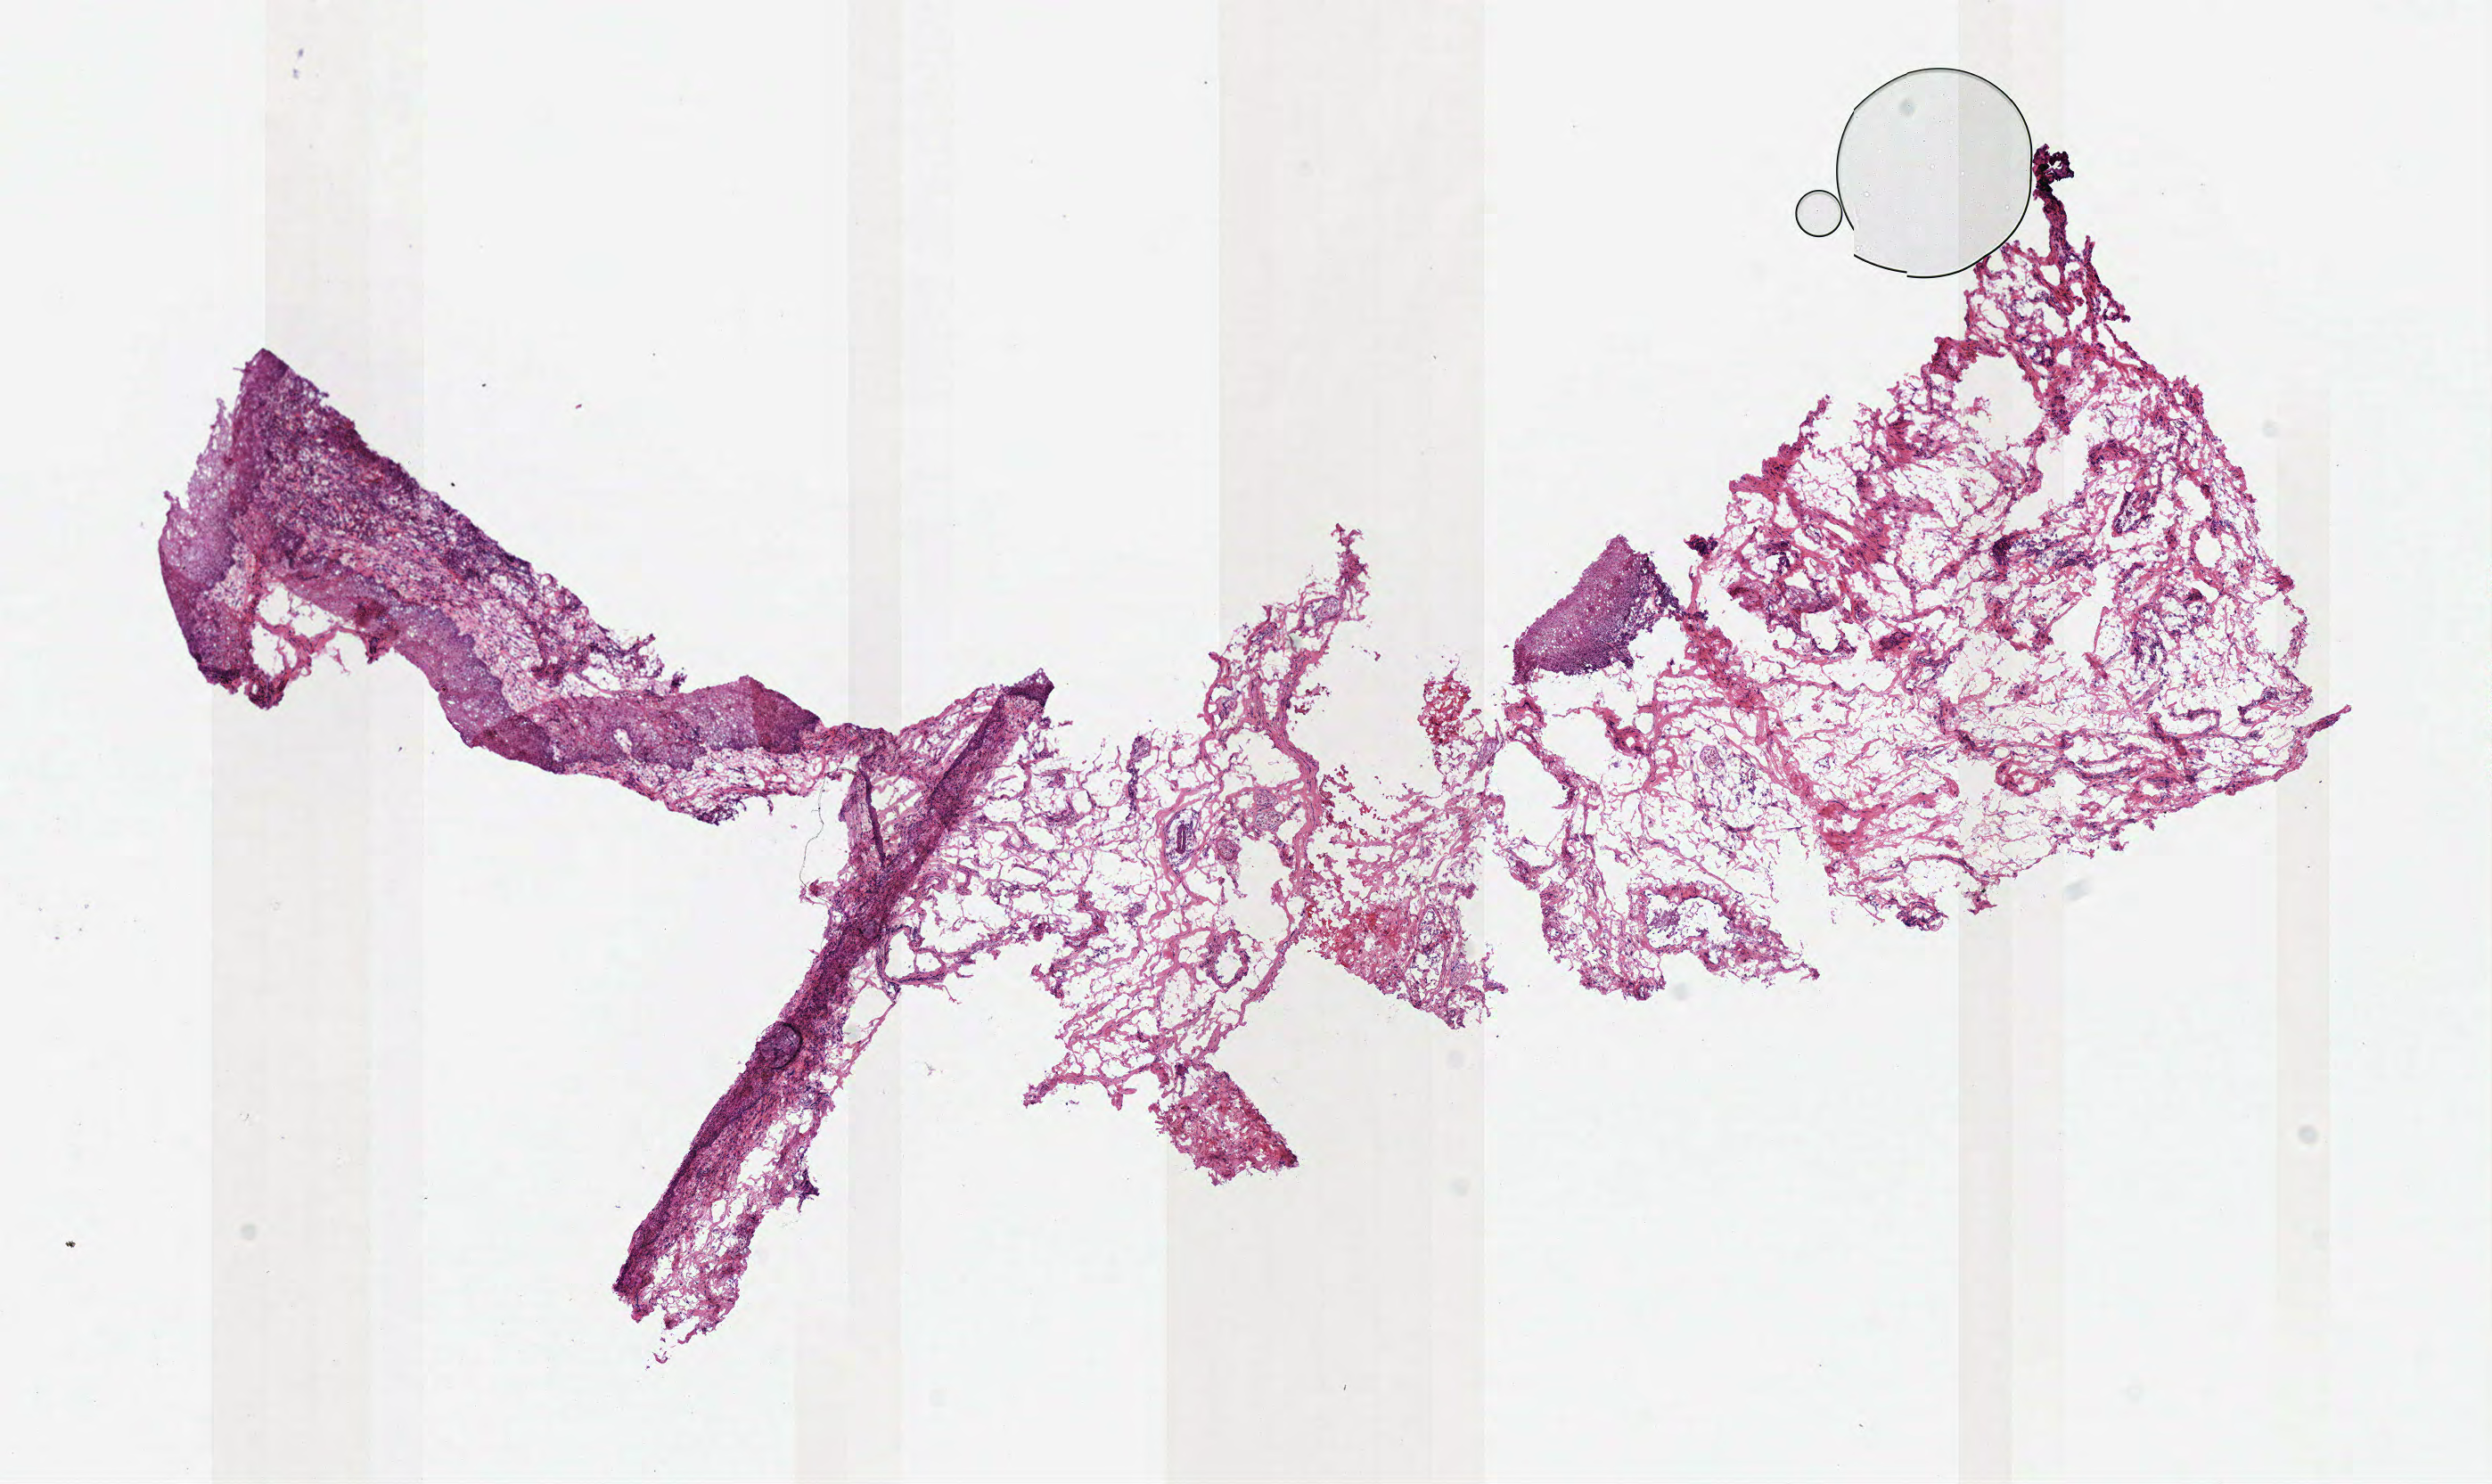
Digitized Hematoxylin and eosin (H&E) stained tissue section (whole slide), whole scanned area (about 11.0 x 6.6 mm, from a 40x scan) shown as a low-resolution overview; frozen section from the top of the tissue portion; solid tissue normal (non-tumour tissue) sample from the head and neck. Male patient; age at initial diagnosis 65 years.
This section: solid tissue normal (non-tumour) sample from the same patient. Patient diagnosis: Squamous cell carcinoma, NOS (larynx, NOS).